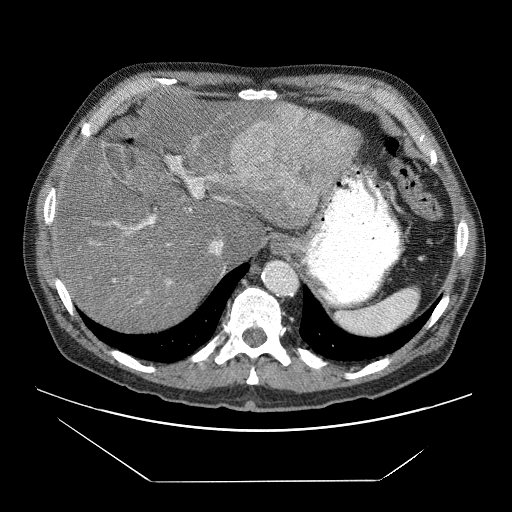
Contrast-enhanced abdominal CT (liver protocol), one axial slice. Slice 53 of 83 in the series (ordered by position). 120 kVp. Soft-tissue window (W 400 / L 40 HU). 512 × 512 image matrix, field of view 420 × 420 mm. From the clinical record (not read from this slice): diagnosis: hepatocellular carcinoma (patient treated with transarterial chemoembolisation; whether this scan precedes or follows treatment is not stated here); TNM stage (as recorded): Stage-IVB; Child-Pugh class: B; tumour nodularity: uninodular.
Outlined on this slice (semi-automatically segmented with operator editing):
- liver parenchyma outside the tumour (the mass and vessels are separate outlines, so this box may not span the whole liver): bounding box (x1, y1, x2, y2) in pixels: (52, 84, 360, 328)
- mass: (233, 103, 358, 224)
- liver vessels: (91, 153, 241, 303)